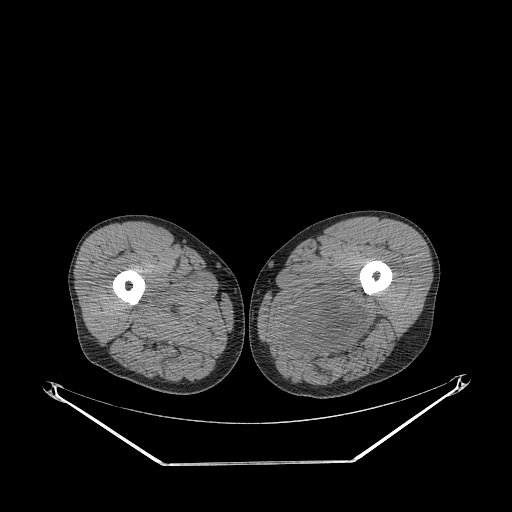
CT of an extremity soft-tissue mass (from a PET/CT study), one axial slice. Position 257 of 267 along the scan axis. 140 kVp. Soft-tissue window (W 400 / L 40 HU). 512 × 512 image matrix. Male patient. From the clinical record (not read from this slice): histological type: undifferentiated pleomorphic liposarcoma; grade: high; site of the primary tumour: left thigh.
Annotated regions visible in this slice (expert contour drawn on MRI and transferred to this co-registered scan by the dataset authors):
- gross tumour volume including surrounding oedema: bounding box [x1, y1, x2, y2] px = [283, 295, 366, 357]
- gross tumour volume (mass): [288, 297, 357, 353]